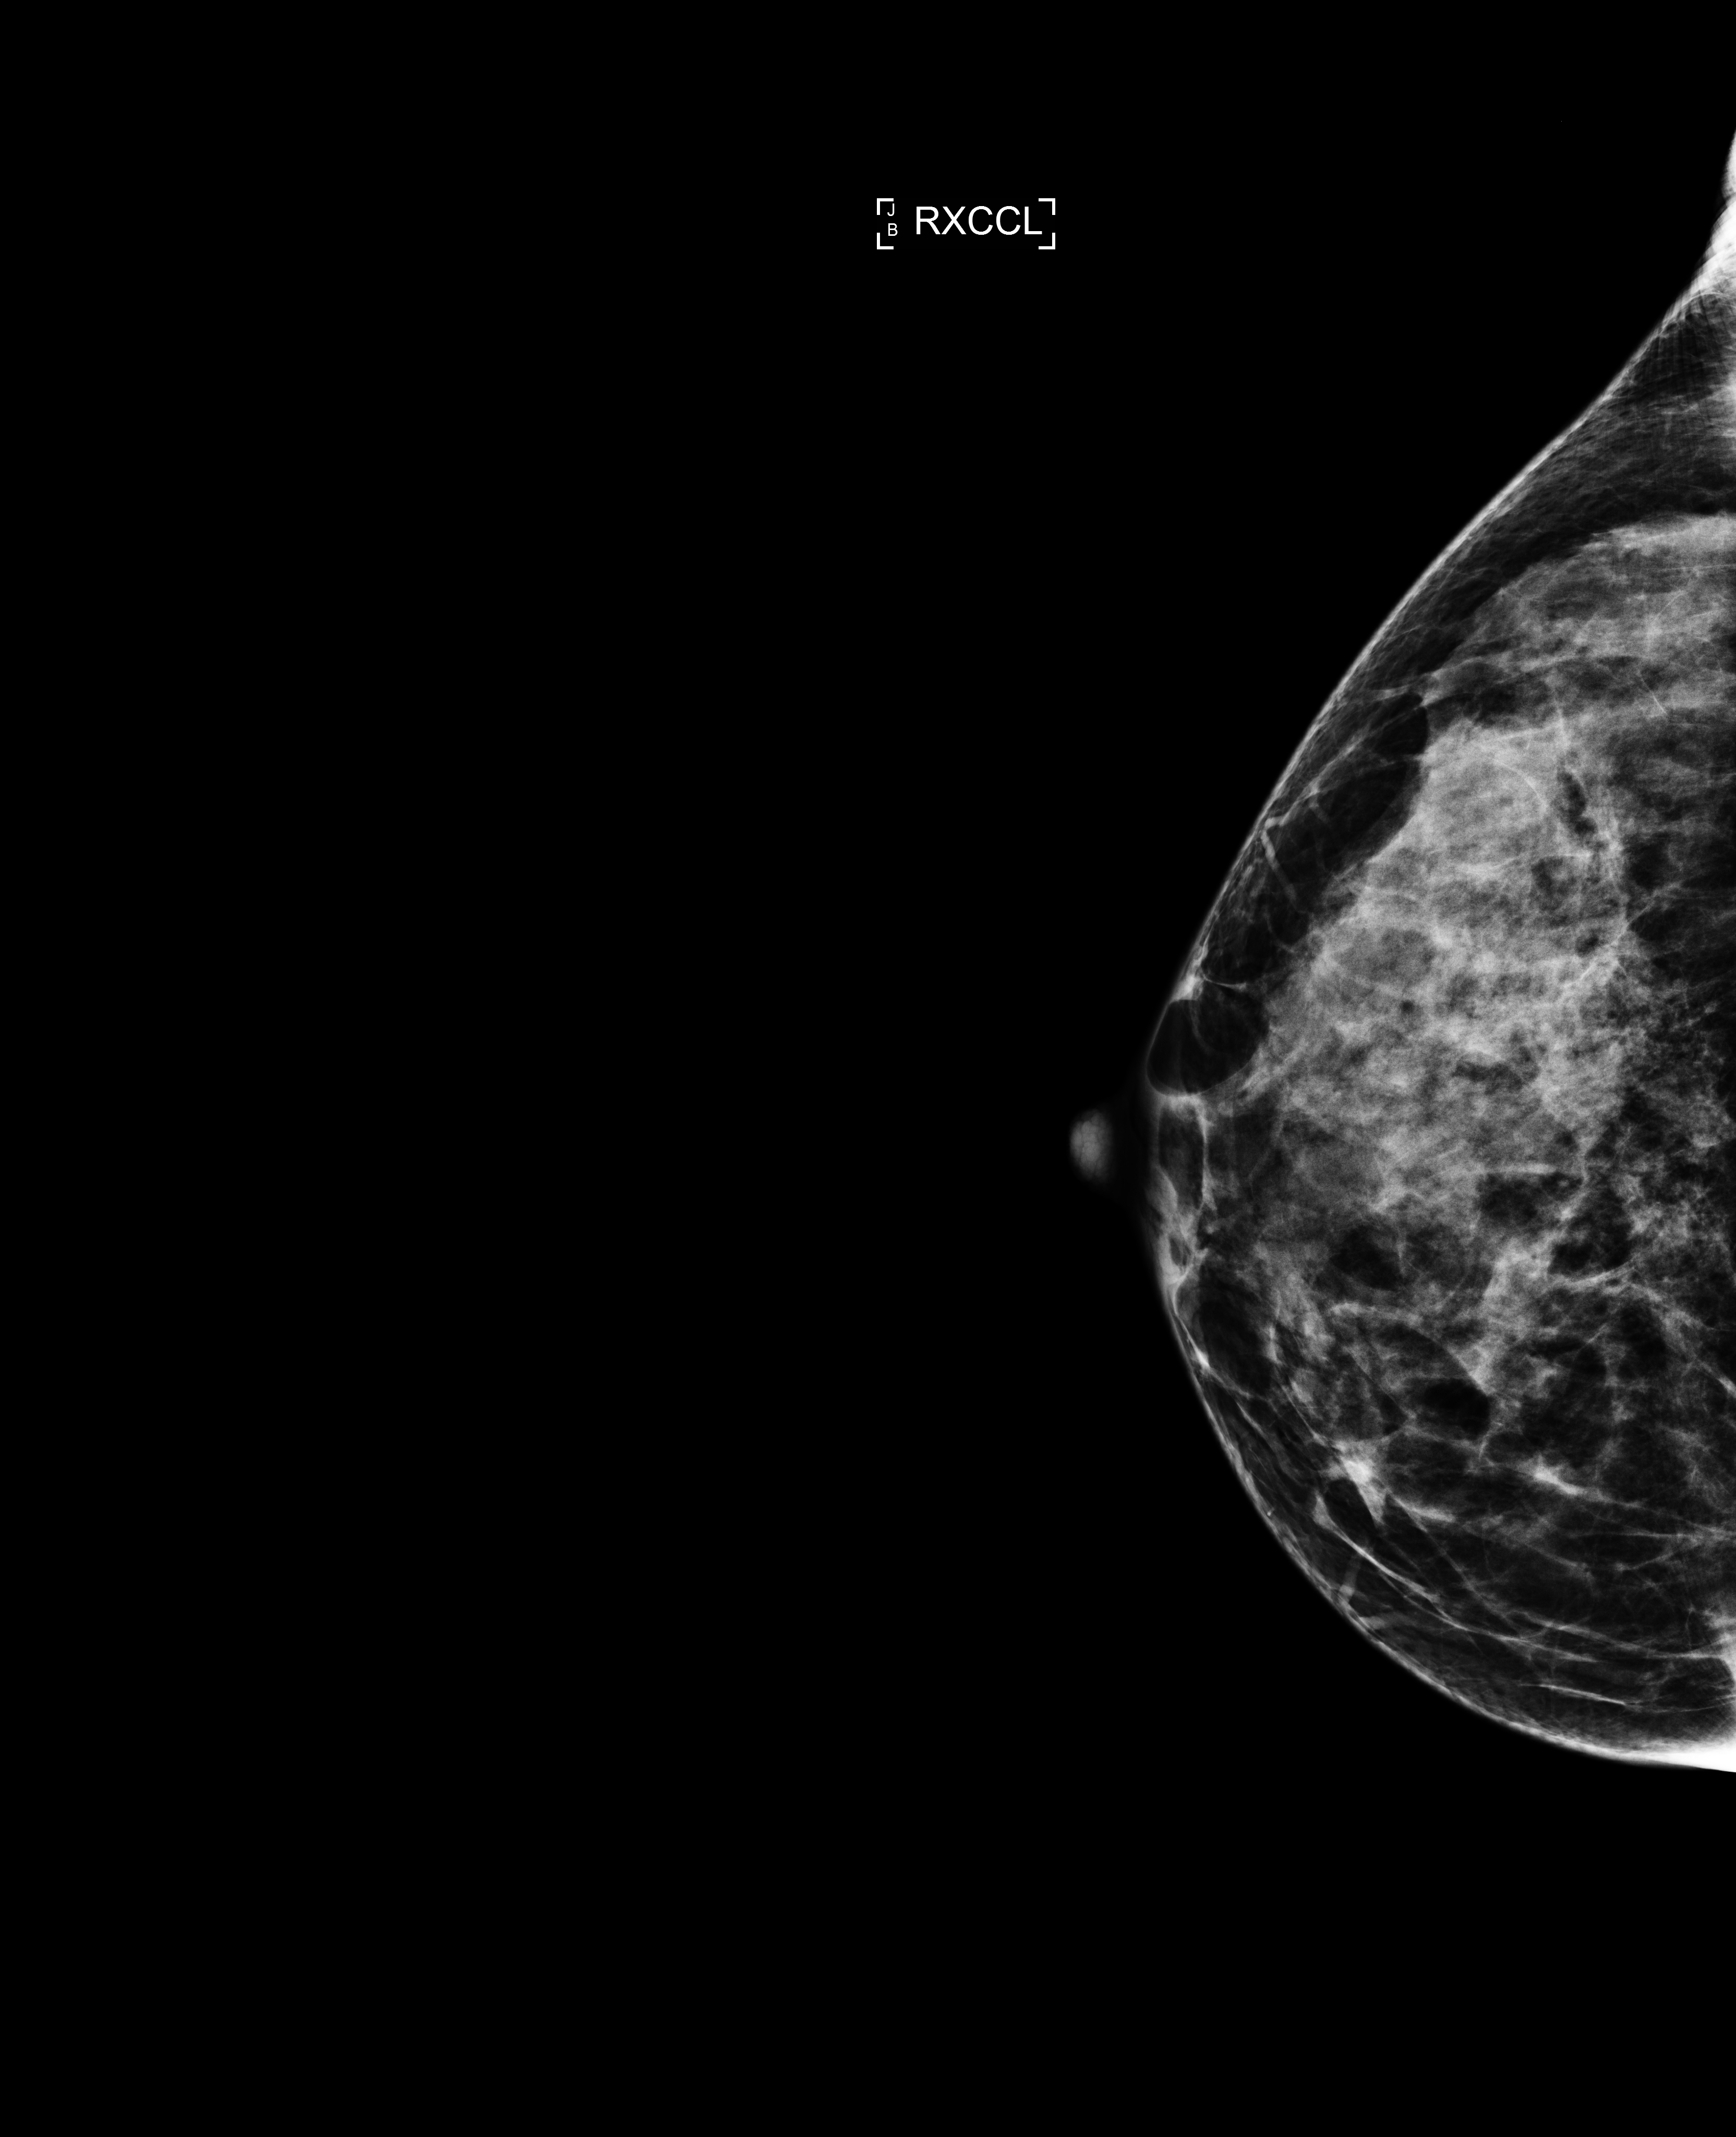
Annual screening mammography examination; compressed breast thickness 63 mm. Patient aged 42 years (female).
Image type: full-field digital mammogram. Breast: right. Projection: exaggerated CC view (lateral).